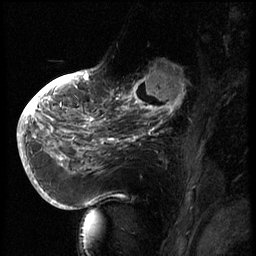
Breast MRI (dynamic contrast-enhanced), one sagittal slice. Slice 25 of 66 in the series (ordered by position). 3 images stored at this slice position (order not interpretable as contrast timing). 1.5 T. TE 4.2 ms, TR 8.9 ms. 2.5 mm slice thickness. 256 × 256 image matrix, field of view 200 × 200 mm. Female patient, age 56 years. From the clinical record (not read from this slice): setting: breast cancer imaged before/during neoadjuvant chemotherapy.
Annotated regions visible in this slice (semi-automatic segmentation, software-assisted and operator-edited):
- analysis volume of interest (the breast-tissue region the enhancement analysis was run in; not a lesion): bounding box (x1, y1, x2, y2) in pixels: (129, 62, 194, 127)
- tumour enhancement mask (voxels above the 140 % enhancement threshold inside the analysis volume of interest): (129, 64, 187, 127)